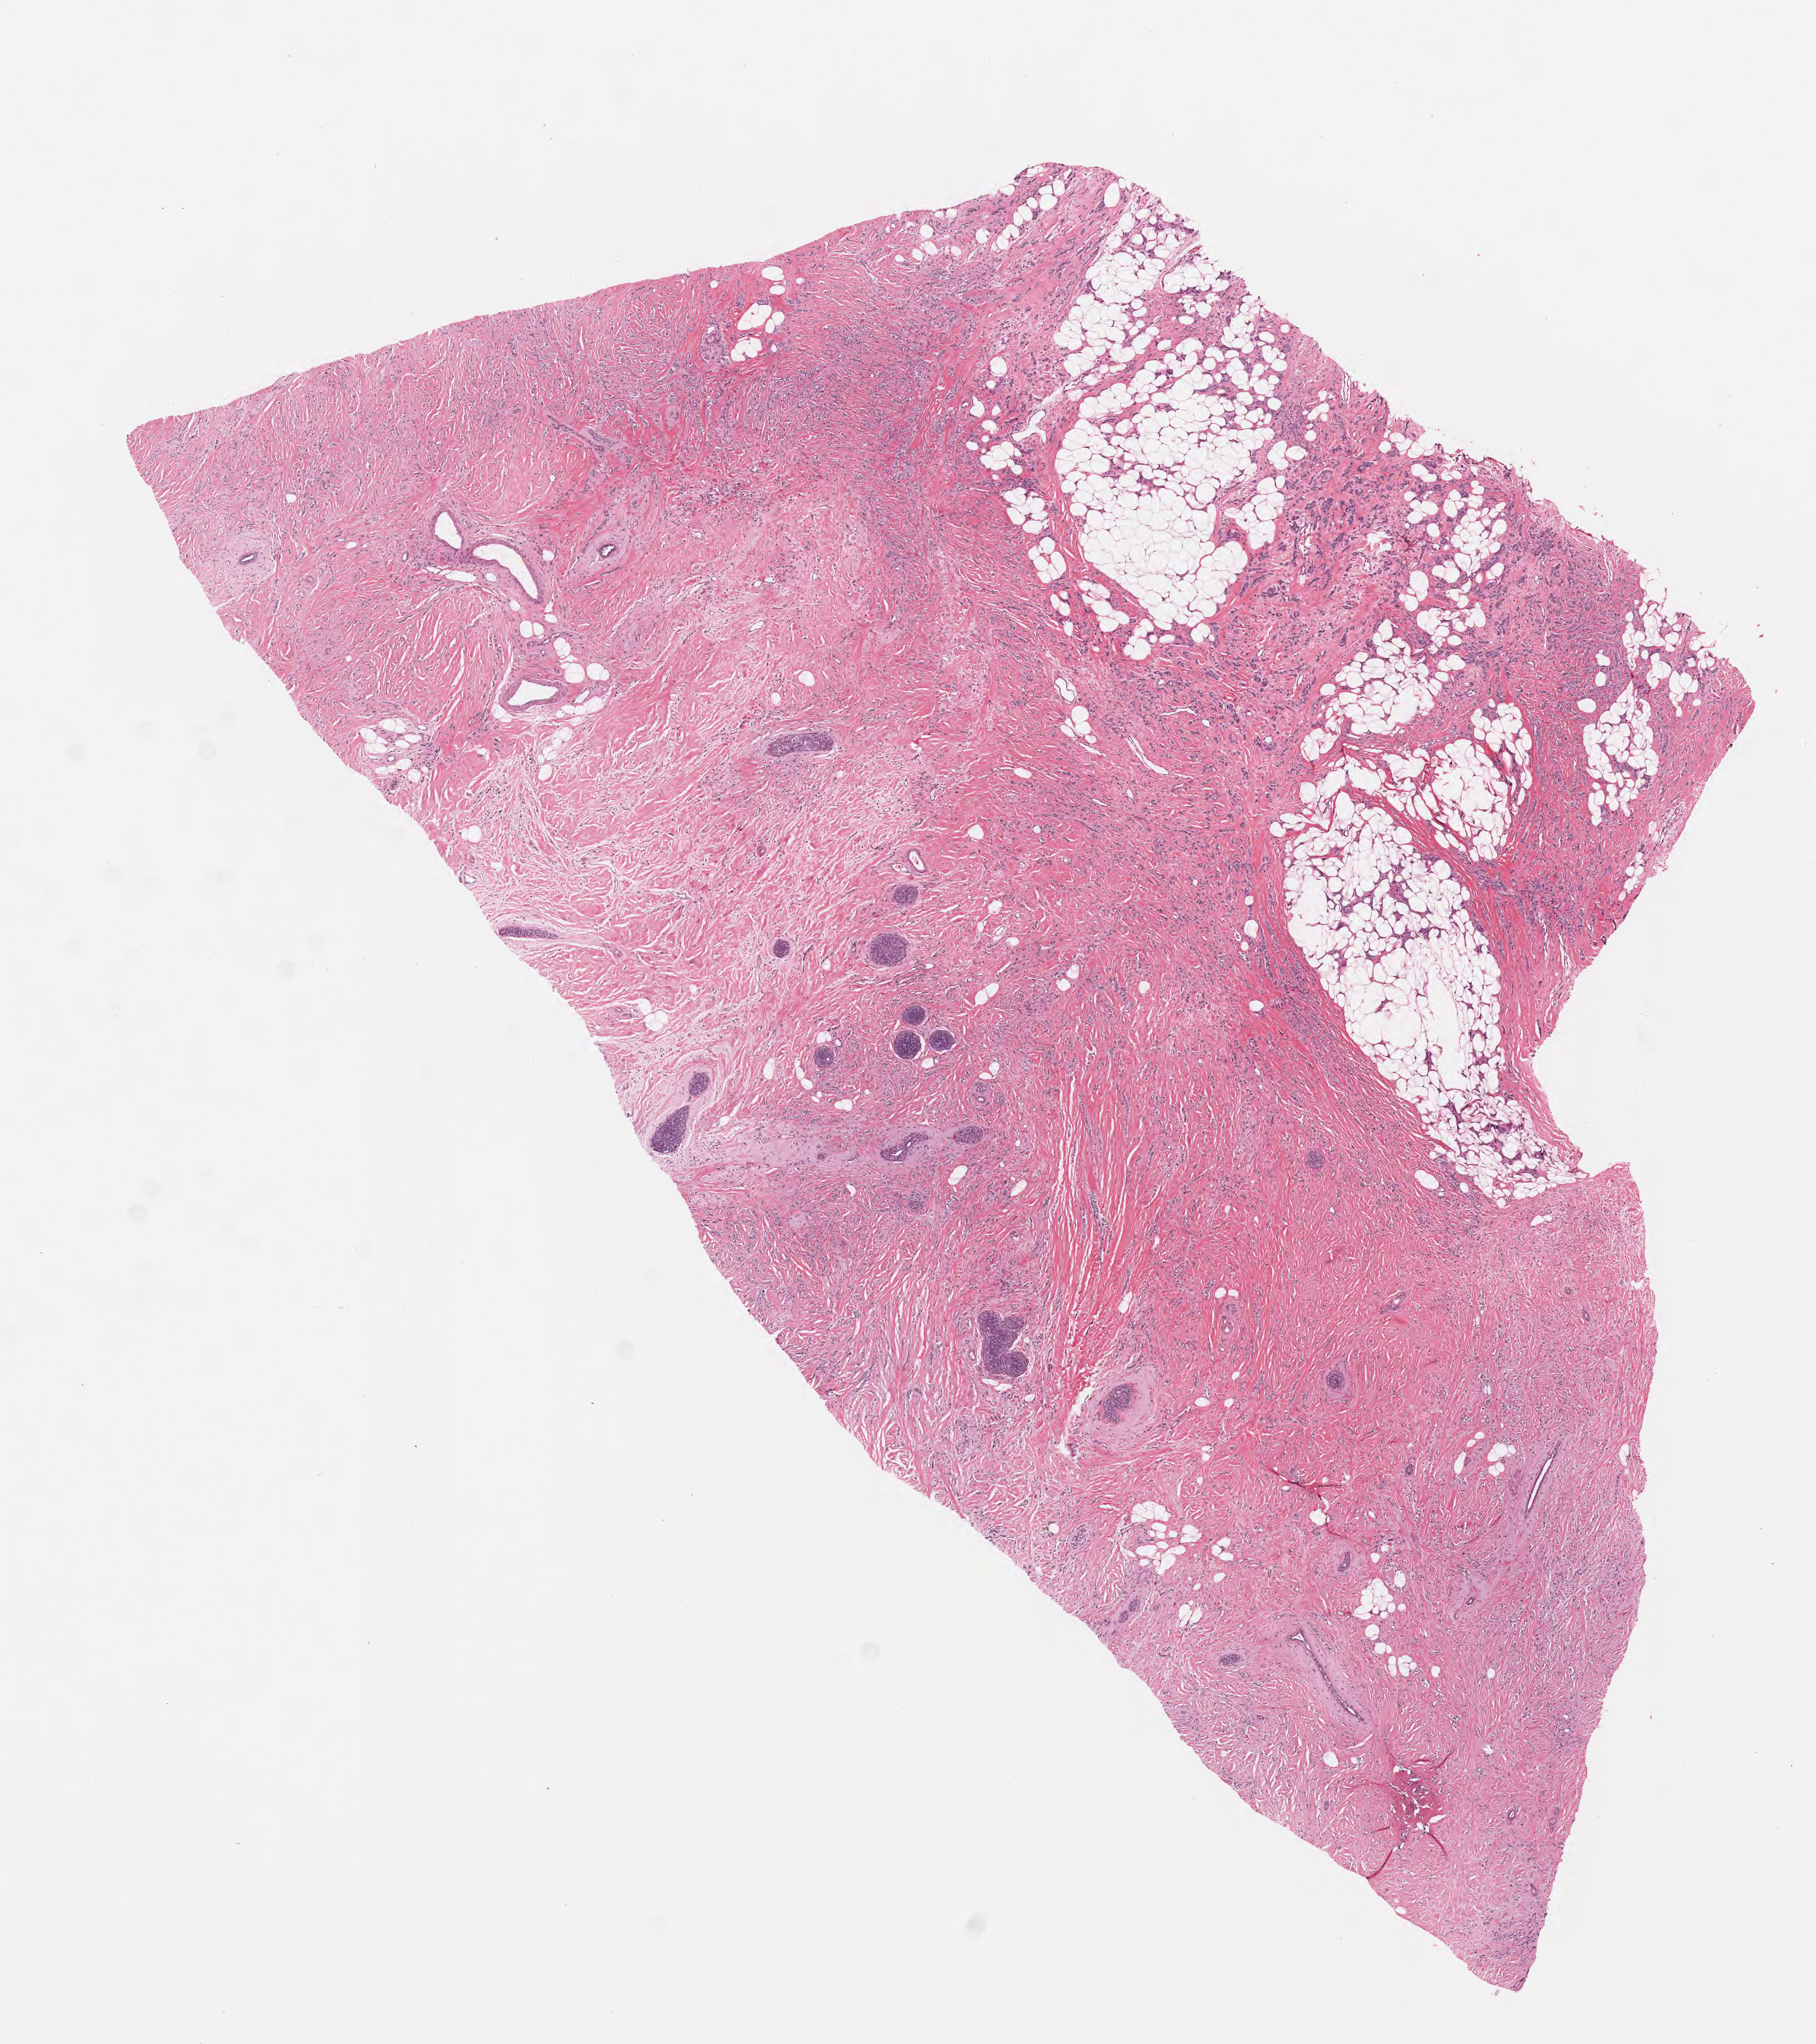
Haematoxylin and eosin whole-slide image, shown as a low-resolution overview of the whole scanned area (about 10.1 x 11.3 mm). Formalin-fixed paraffin-embedded section. Specimen: primary tumor. Anatomic site: breast. Patient: female, age at initial diagnosis 62 years. Tumor grade: G2 (moderately differentiated). Pathologist review of this section (percent, as recorded): tumor cells 40%, tumor nuclei 50%, stromal cells 40%, necrosis 0%, normal cells 20%. Inflammatory infiltration, as recorded: lymphocyte infiltration 0%, monocyte infiltration 0%, neutrophil infiltration 0%.
Diagnosis: Lobular carcinoma, NOS. AJCC pathologic stage: Stage IIB.